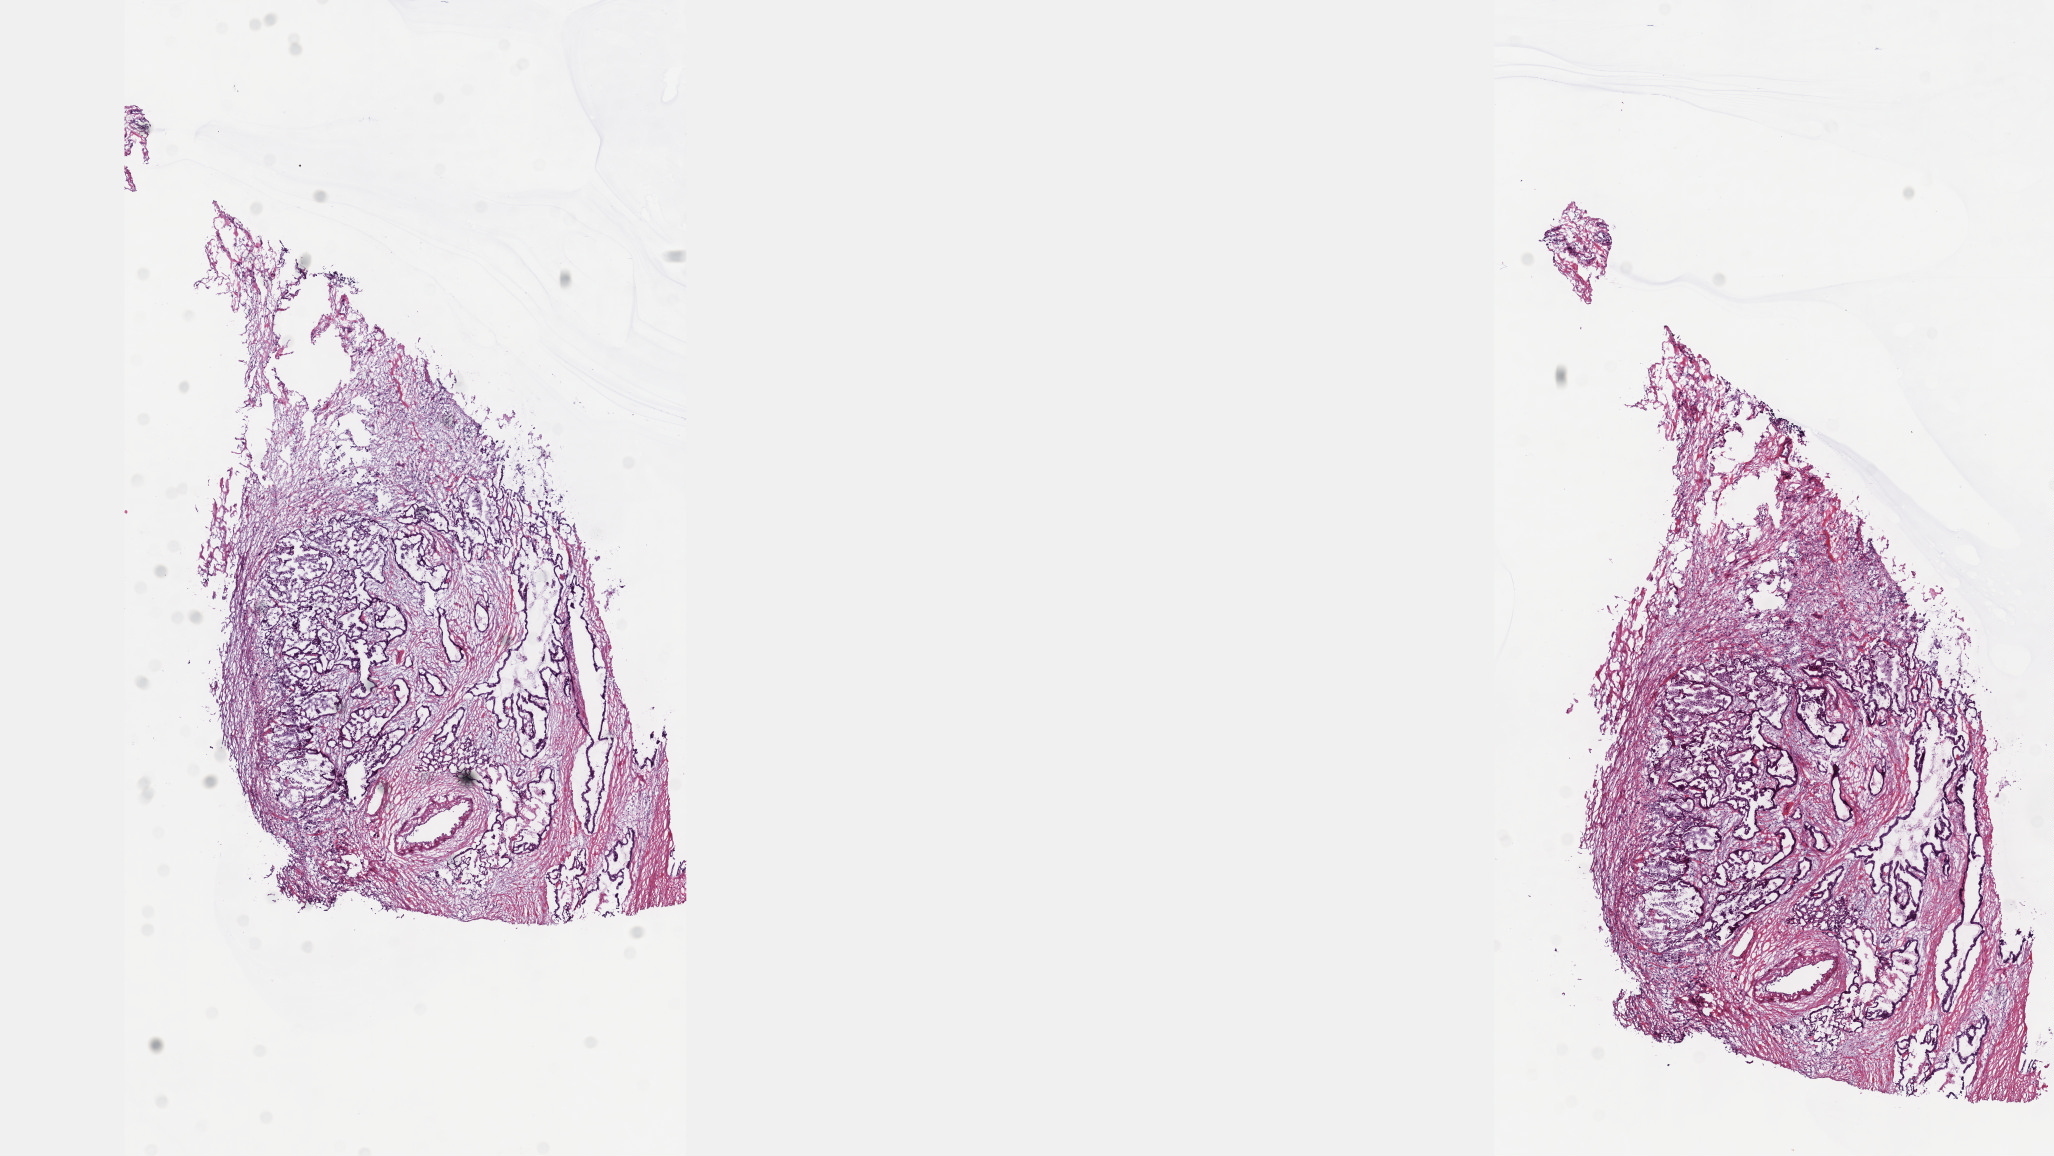
Whole-slide histology image, H&E, whole scanned area (about 16.6 x 9.3 mm) shown as a low-resolution overview. Frozen section from the top of the tissue portion. Primary tumour sample from the pancreas. Female, age 64 years at initial diagnosis. Histologic grade: G1 (well differentiated). Slide review estimates, as recorded: tumour cells 40%, tumour nuclei 50%, normal cells 0%, stromal cells 60%, necrosis 0%. Infiltration values recorded for this section: lymphocyte infiltration 0%, monocyte infiltration 0%, neutrophil infiltration 0%.
TNM: T3 N1 MX. AJCC pathologic stage: IB (7th edition). Pathologic diagnosis: Infiltrating duct carcinoma, NOS. Lymph nodes positive (case pathology): 9 of 26 examined.